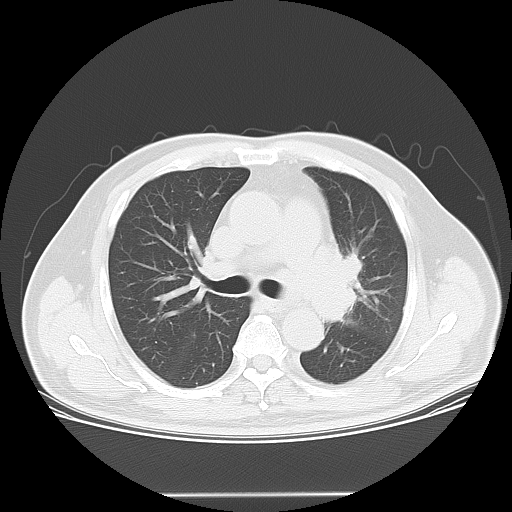
Chest CT, one axial slice; position 36 of 55 along the scan axis; reconstruction kernel LUNG; 120 kVp; lung window (W 1500 / L -600 HU); 5 mm slice thickness; 512 × 512 image matrix, field of view 398 × 398 mm. Patient: male, 61 years. Case-level facts recorded for this patient, not image findings: clinical TNM (as recorded): T3 N1 M1.
Outlined on this slice (bounding box drawn by a radiologist):
- lung tumour (recorded histology: small cell carcinoma): bounding box (x1, y1, x2, y2) in pixels: (320, 238, 375, 332)